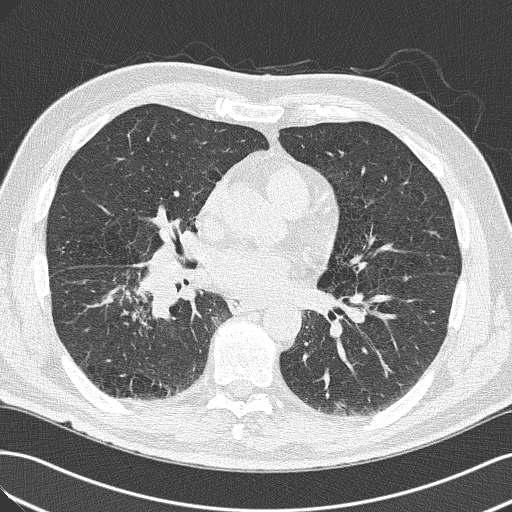
Low-dose screening chest CT, axial slice. Baseline annual screen. Lung window (W 1500 / L -600 HU). 2 mm slice thickness. Slice 84 of 143 in the series. Male, age 65 years at enrolment. Current smoker at enrolment.
Lesion marked by an expert reader, bounding box (x1, y1, x2, y2) in pixels: (103, 255, 209, 341). The exam's reader record, not a measurement of the box and not confirmed to be the same lesion: non-calcified nodule or mass ≥4 mm, right upper lobe, 18 × 13 mm, spiculated (stellate) margins, soft tissue attenuation. Later outcome: lung cancer diagnosed 14 days after this screen — adenocarcinoma, NOS, right lower lobe, poorly differentiated (G3), stage IIIA (AJCC 6th edition), 40 mm at pathology.